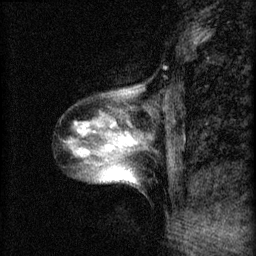
Breast MRI (dynamic contrast-enhanced), one sagittal slice. Slice 16 of 60 in the series (ordered by position). 3 images stored at this slice position (order not interpretable as contrast timing). 1.5 T. TE 4.2 ms, TR 8.2 ms. 2 mm slice thickness. 256 × 256 image matrix, field of view 180 × 180 mm. Patient: female, 40 years.
Structures marked on this image (semi-automatically segmented with operator editing):
- analysis volume of interest (the breast-tissue region the enhancement analysis was run in; not a lesion): bounding box [x1, y1, x2, y2] px = [64, 84, 152, 189]
- tumour enhancement mask (voxels above the 70 % enhancement threshold inside the analysis volume of interest): [85, 124, 138, 149]